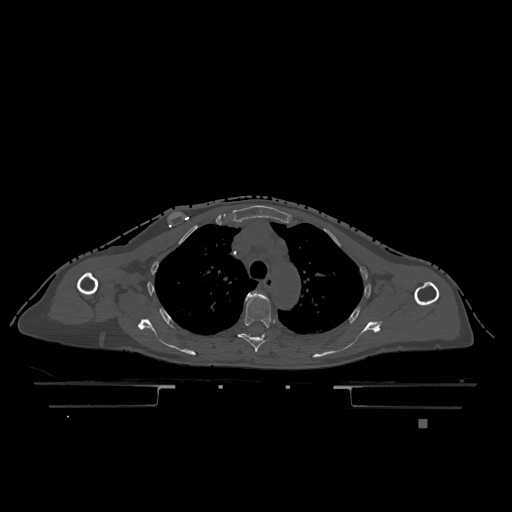
CT including the spine, one axial slice; bone window (W 1800 / L 400 HU); 0.5 mm slice thickness; 512 × 512 image matrix. Patient: female, 74 years. Case-level facts recorded for this patient, not image findings: primary cancer: lung.
Outlined on this slice (semi-automatic segmentation, software-assisted and operator-edited):
- T4 vertebra: bounding box <238,291,275,353> (left, top, right, bottom; pixels)